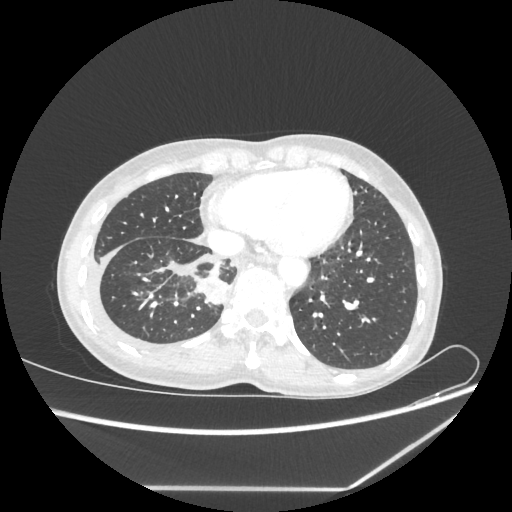
Chest CT, one axial slice. Slice 64 of 237 in the series (ordered by position). 80 kVp. Lung window (W 1500 / L -600 HU). 512 × 512 image matrix, field of view 364 × 364 mm. Female patient, age 59 years. From the clinical record (not read from this slice): clinical TNM (as recorded): T1c N1 M1.
Annotated regions visible in this slice (bounding box drawn by a radiologist):
- lung tumour (recorded histology: adenocarcinoma): bounding box <195,274,228,306> (left, top, right, bottom; pixels)